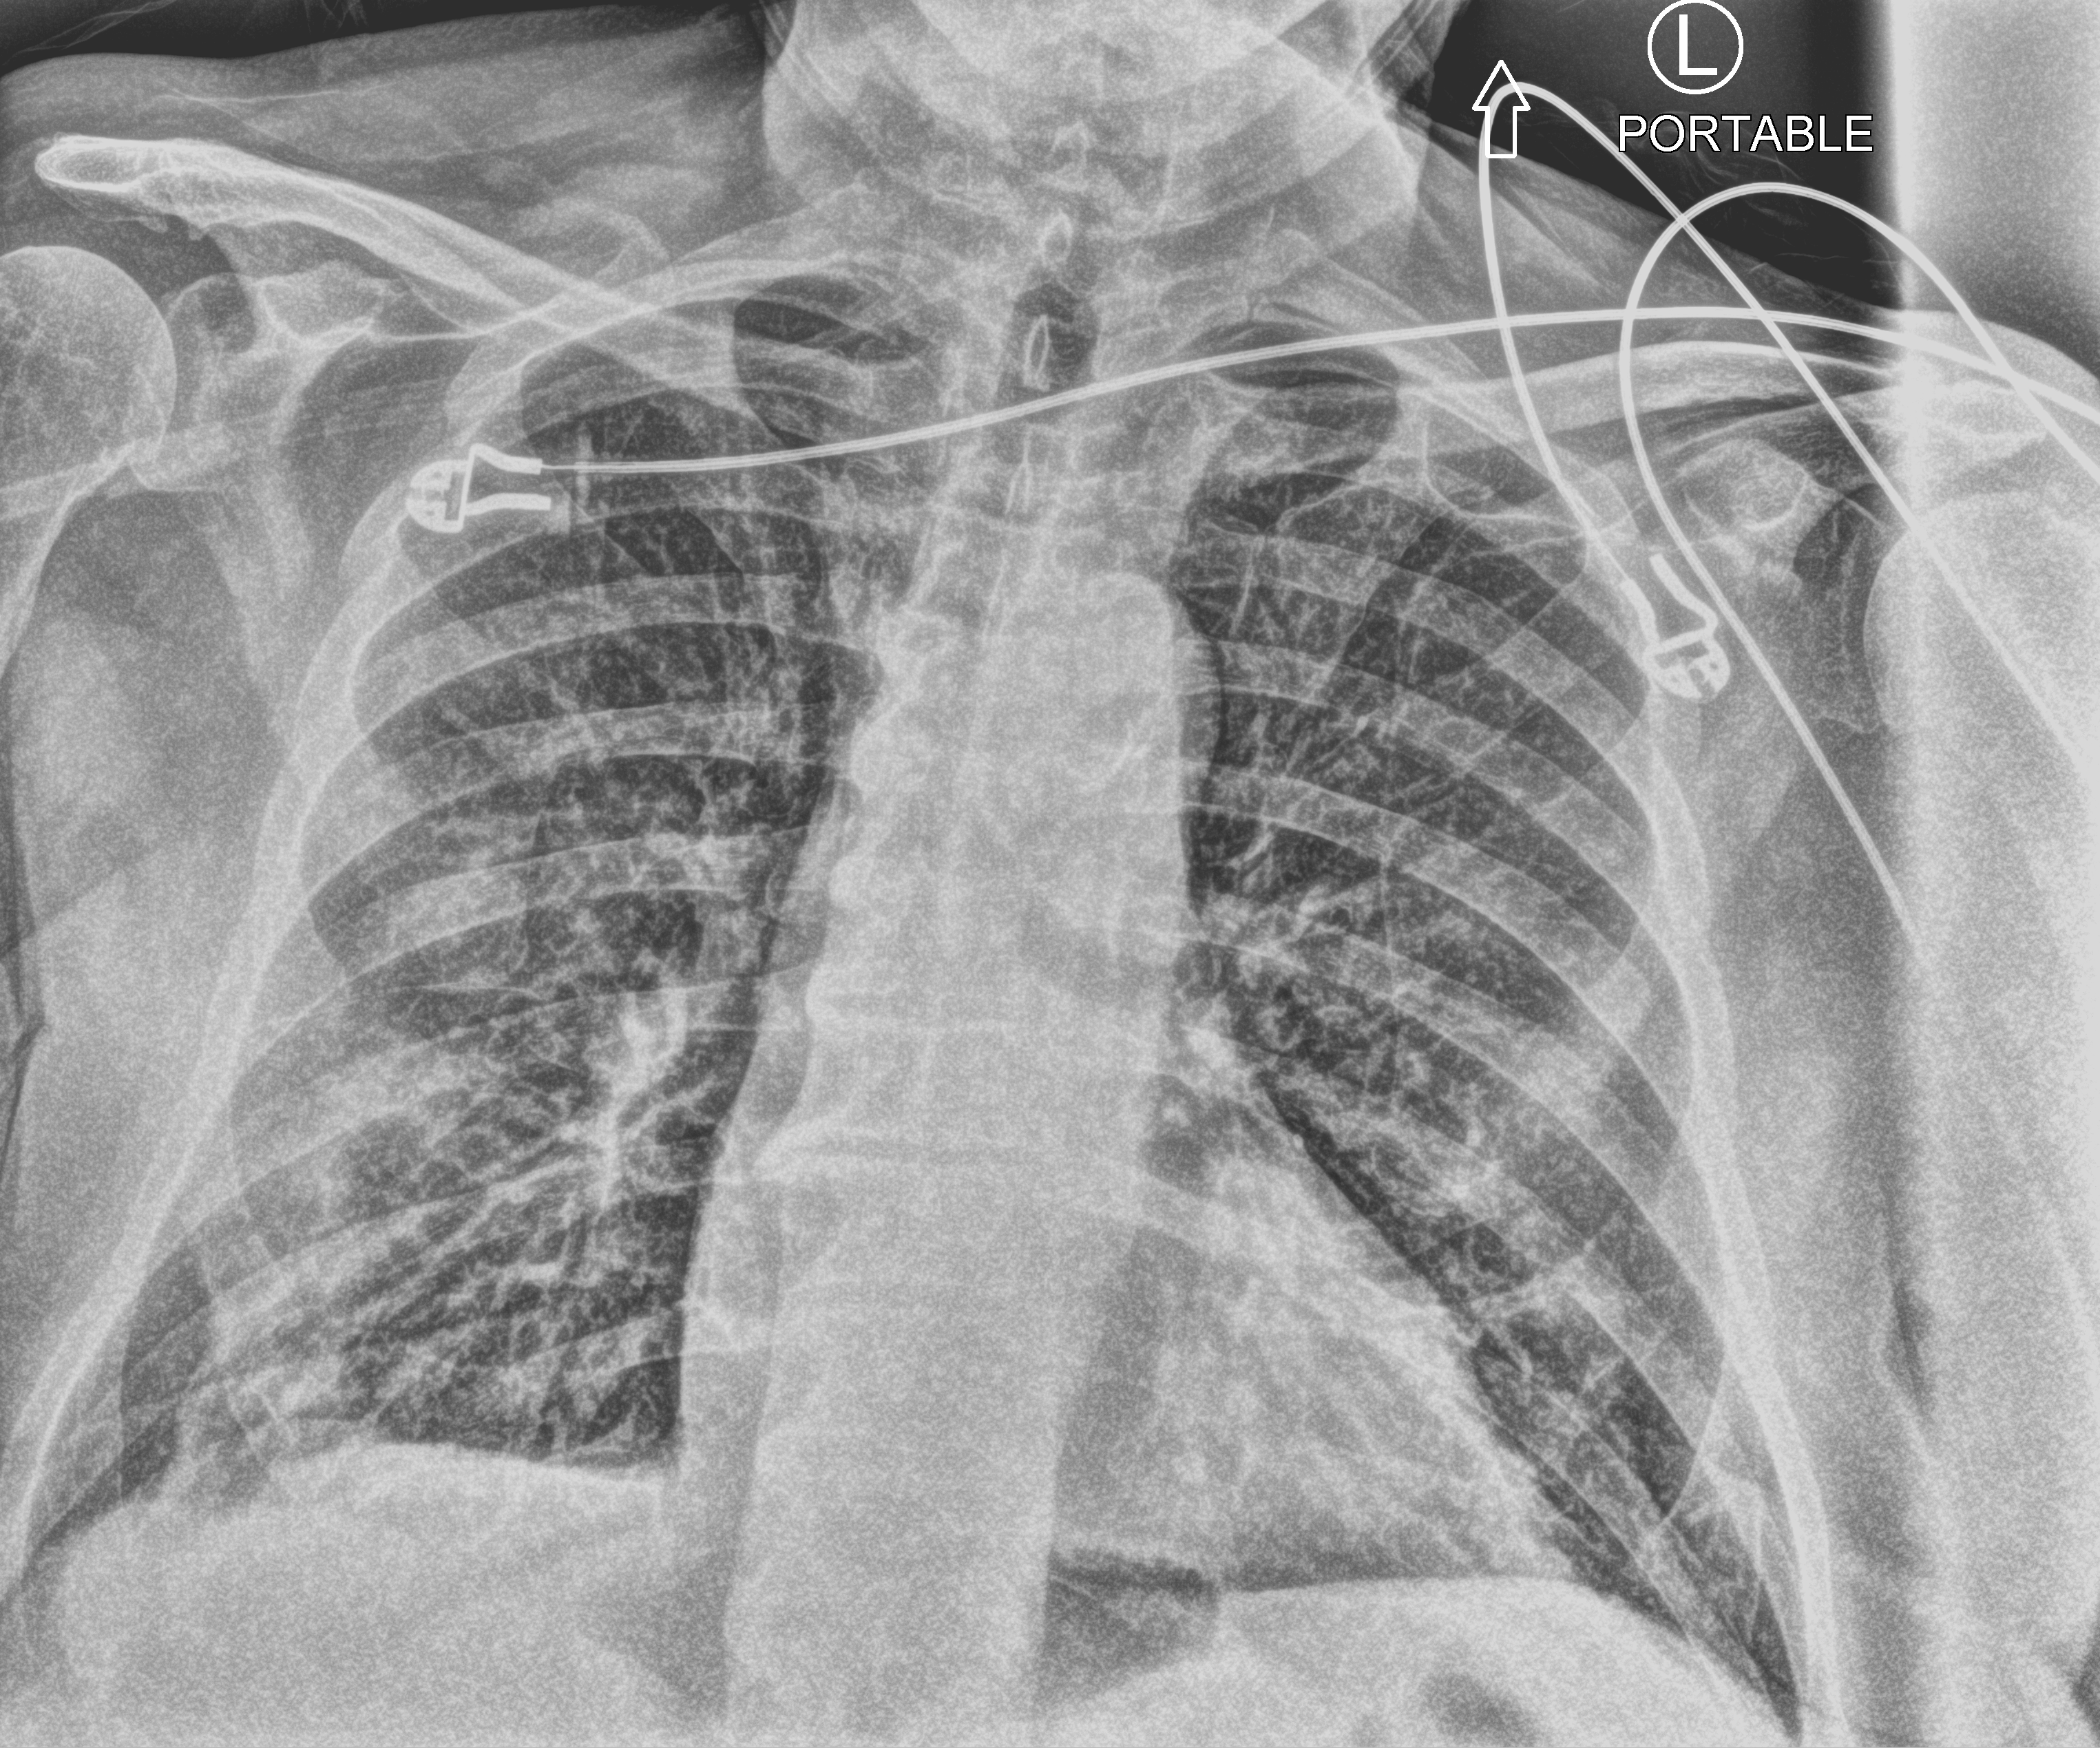
Chest X-ray (portable); anteroposterior (AP) projection. Patient hospitalised with COVID-19; male, aged 75–90 years.
Hospital-stay facts (about this admission, not read from this image; timing relative to this image not recorded): admitted to intensive care during this hospital stay: no; chronic kidney disease (admission record): no.